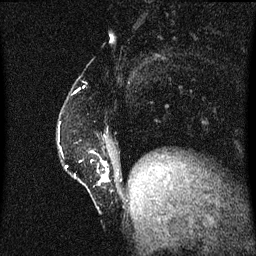
Breast MRI (dynamic contrast-enhanced), one sagittal slice; dynamic contrast-enhanced series, image 2 of 3 at this slice position (ordered by acquisition); 1.5 T; TE 4.2 ms, TR 8.4 ms; 2 mm slice thickness; 256 × 256 image matrix, field of view 200 × 200 mm. Female patient, age 52 years. Case-level facts recorded for this patient, not image findings: setting: breast cancer imaged before/during neoadjuvant chemotherapy; receptor status: HER2-positive.
Structures marked on this image (semi-automatic segmentation, software-assisted and operator-edited):
- analysis volume of interest (the breast-tissue region the enhancement analysis was run in; not a lesion): bounding box [x1, y1, x2, y2] px = [67, 142, 112, 195]
- tumour enhancement mask (voxels above the 70 % enhancement threshold inside the analysis volume of interest): [103, 162, 109, 181]